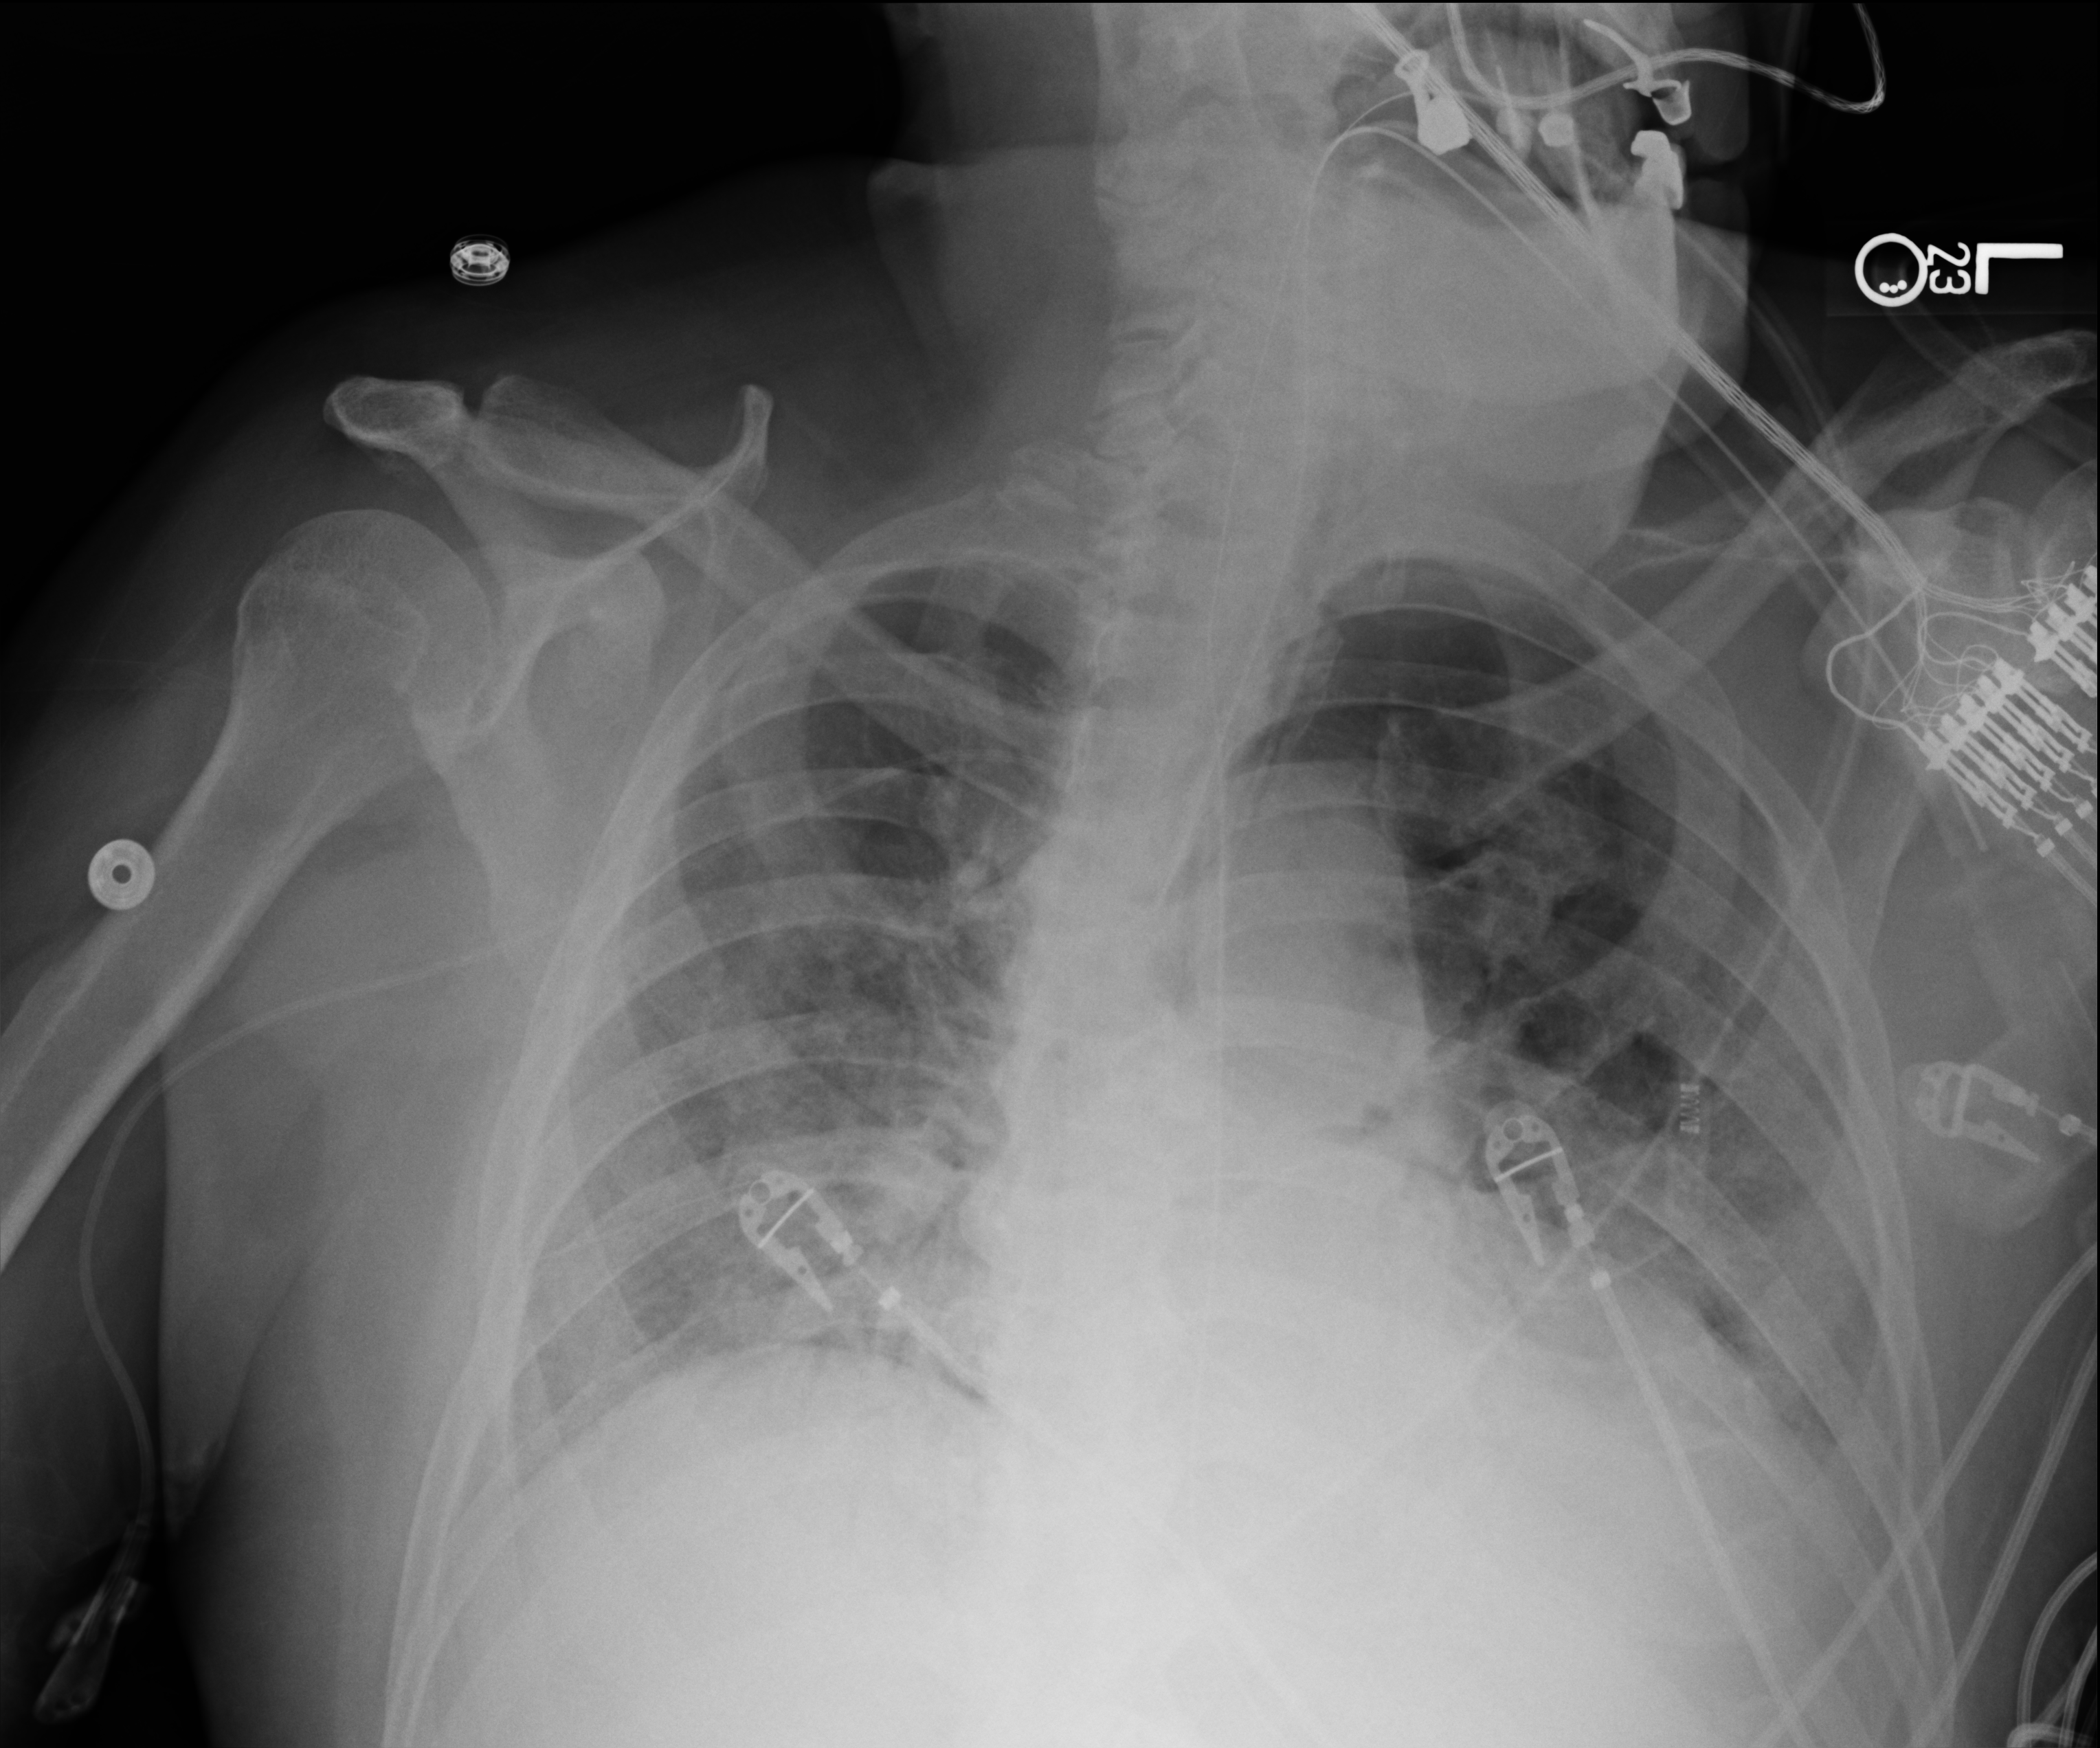
Bedside chest radiograph (computed radiography); anteroposterior (AP) projection. Patient hospitalised with COVID-19; male, aged 75–90 years.
From the hospital-stay record, not from the radiograph (when in the stay this image was taken is not recorded): smoking status (admission record): former; mechanically ventilated during this hospital stay: yes; admitted to intensive care during this hospital stay: yes.